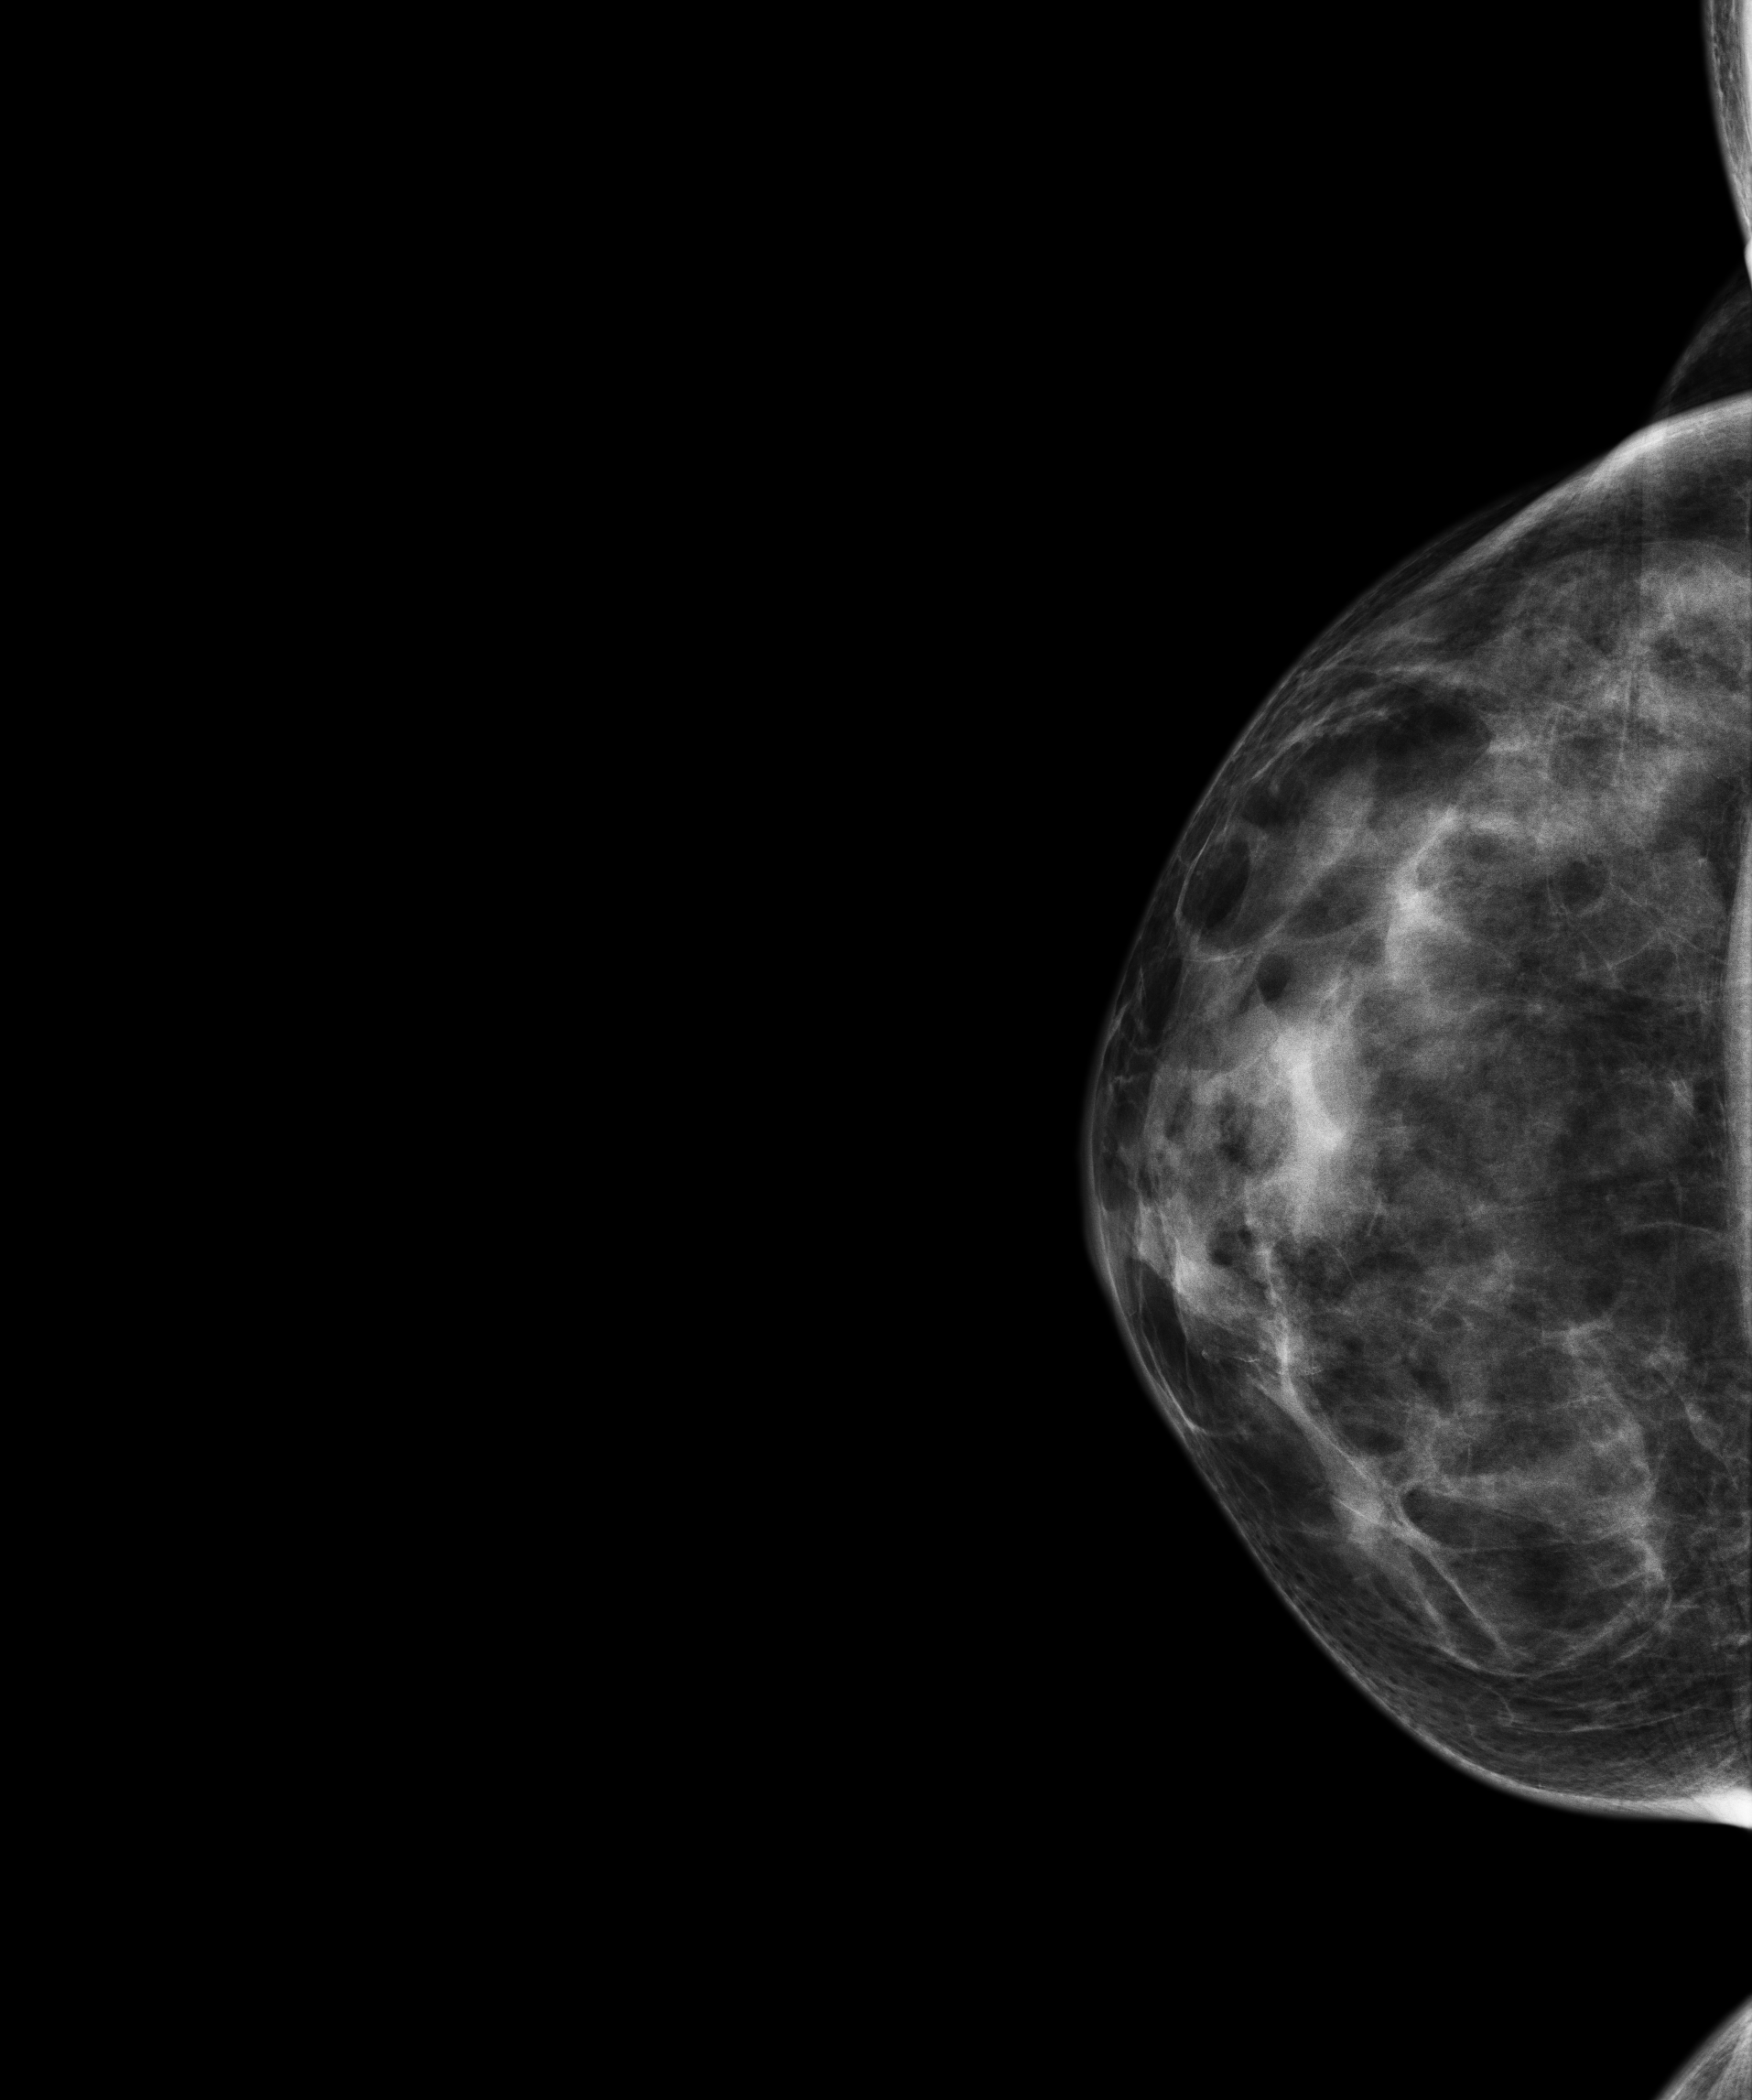
Annual screening mammography examination, system: Senographe Essential ADS_56.21.3. Female patient, age 67 years.
Image type: full-field digital mammogram. Breast: right. Projection: CC view.